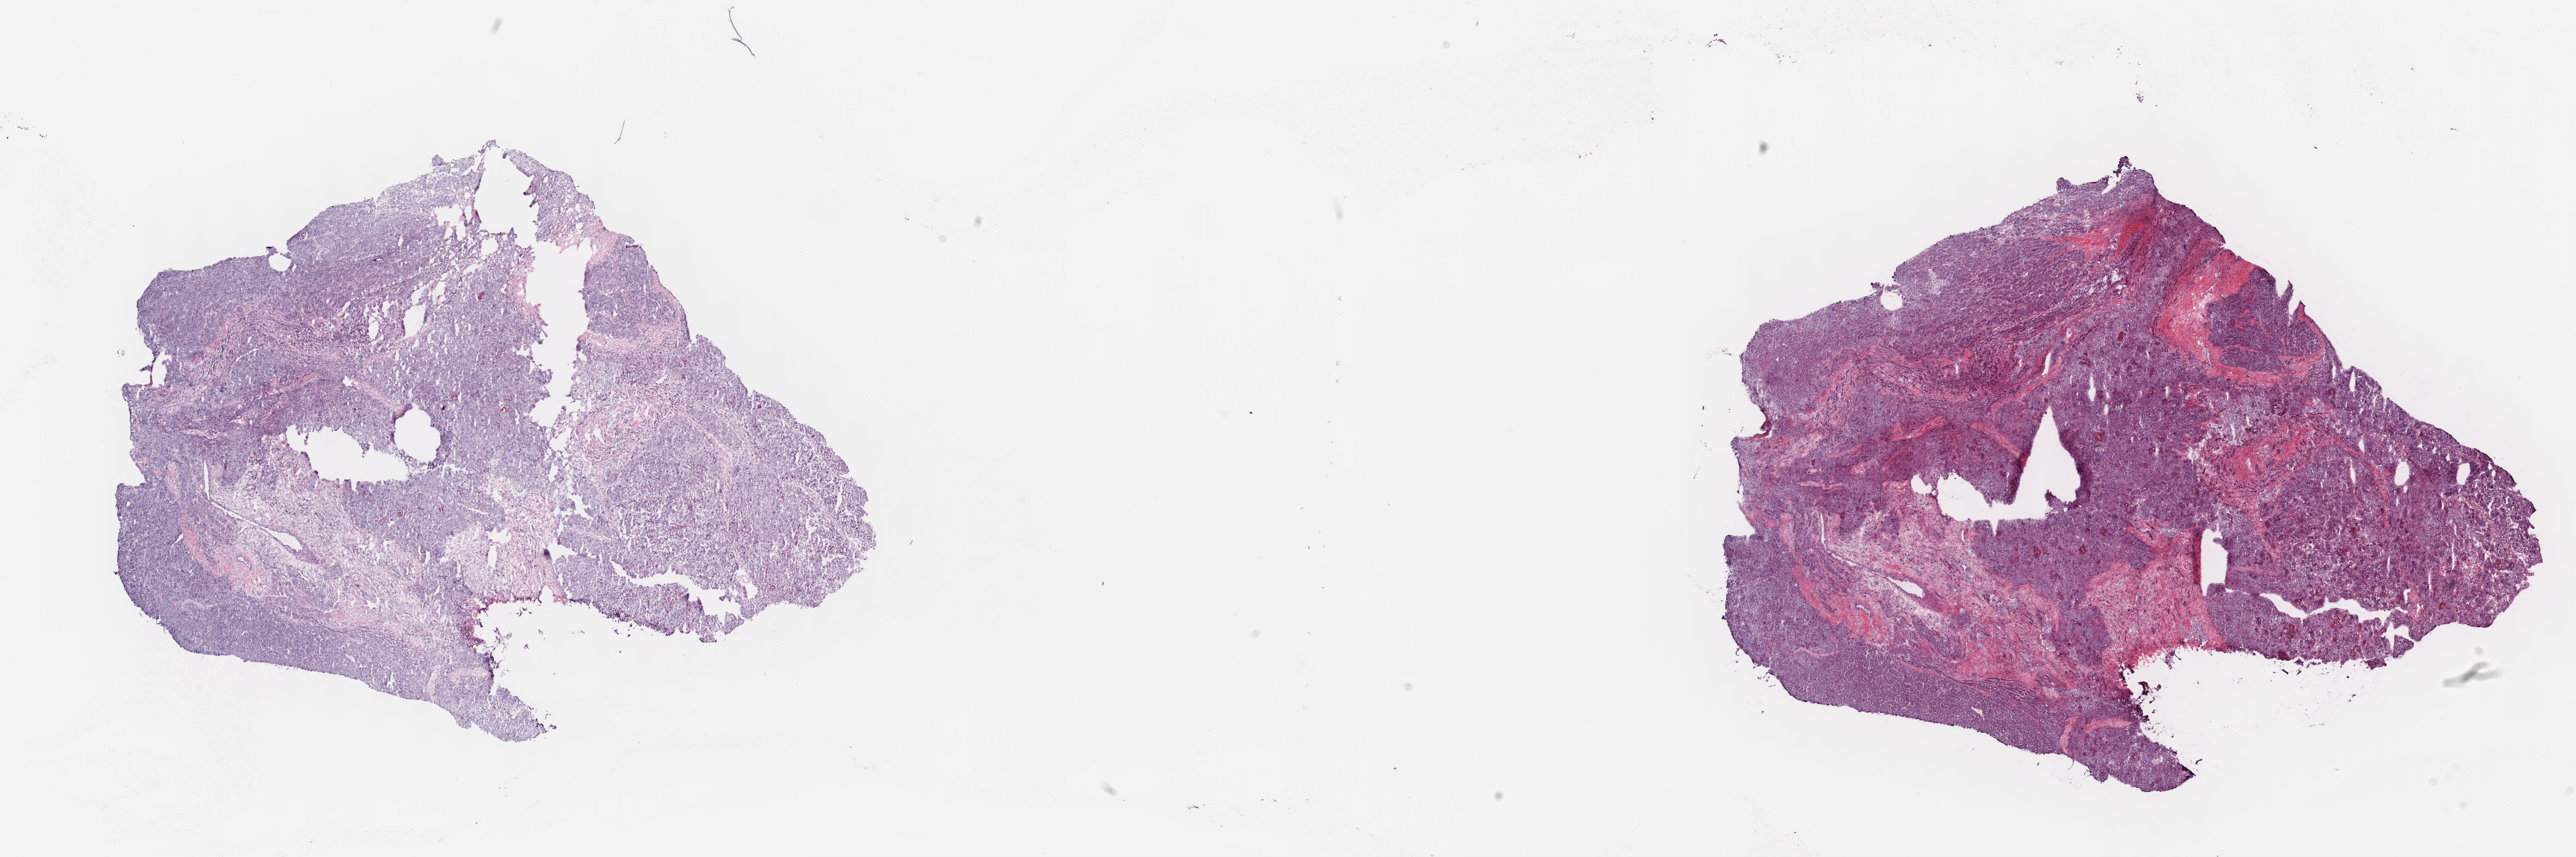
Whole-slide histology image, H&E-stained — whole scanned area (about 29.2 x 9.7 mm, slide scanned at 40x) shown as a low-resolution overview; frozen section from the top of the tissue portion; liver, primary tumour sample. Male patient; age at initial diagnosis 67 years.
Diagnosis: Hepatocellular carcinoma, NOS.